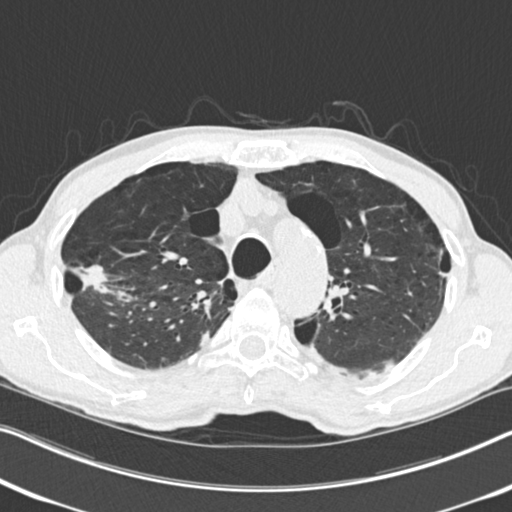
Low-dose screening chest CT, one axial slice; slice 188 of 251 in the series (ordered by position); 120 kVp; lung window (W 1500 / L -600 HU); 2 mm slice thickness; 512 × 512 image matrix.
Annotated regions visible in this slice (manually delineated by an expert):
- lesion 1 (tumor, upper lobe of right lung): bounding box [x1, y1, x2, y2] px = [75, 266, 111, 294]